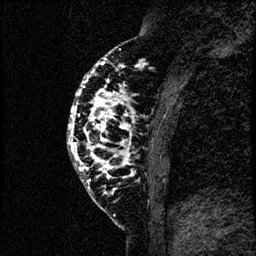
Breast MRI (dynamic contrast-enhanced), one sagittal slice. Position 25 of 60 along the scan axis. Dynamic contrast-enhanced study with each time point stored as its own series, time point 2 of 4 at this slice position (early post-contrast, ordered by acquisition time). 1.5 T. TE 4.2 ms, TR 17.6 ms. 2 mm slice thickness. 256 × 256 image matrix, field of view 200 × 200 mm. Female patient, age 40 years. From the clinical record (not read from this slice): setting: breast cancer imaged before/during neoadjuvant chemotherapy; receptor status: HER2-positive.
Annotated regions visible in this slice (semi-automatically segmented with operator editing):
- analysis volume of interest (the breast-tissue region the enhancement analysis was run in; not a lesion): bounding box [x1, y1, x2, y2] px = [66, 55, 182, 206]
- tumour enhancement mask (voxels above the 100 % enhancement threshold inside the analysis volume of interest): [67, 62, 137, 181]